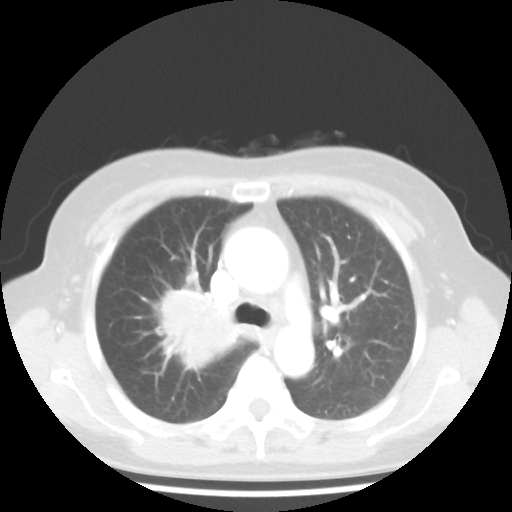
Chest CT, one axial slice; slice 29 of 44 in the series (ordered by position); reconstruction kernel STANDARD; 100 kVp; lung window (W 1500 / L -600 HU); 5 mm slice thickness; 512 × 512 image matrix. Patient: female, 62 years. Case-level facts recorded for this patient, not image findings: clinical TNM (as recorded): T3 N0 M0; histopathological grade: G3.
Annotated regions visible in this slice (bounding box drawn by a radiologist):
- lung tumour (recorded histology: small cell carcinoma): bounding box (x1, y1, x2, y2) in pixels: (155, 284, 248, 376)